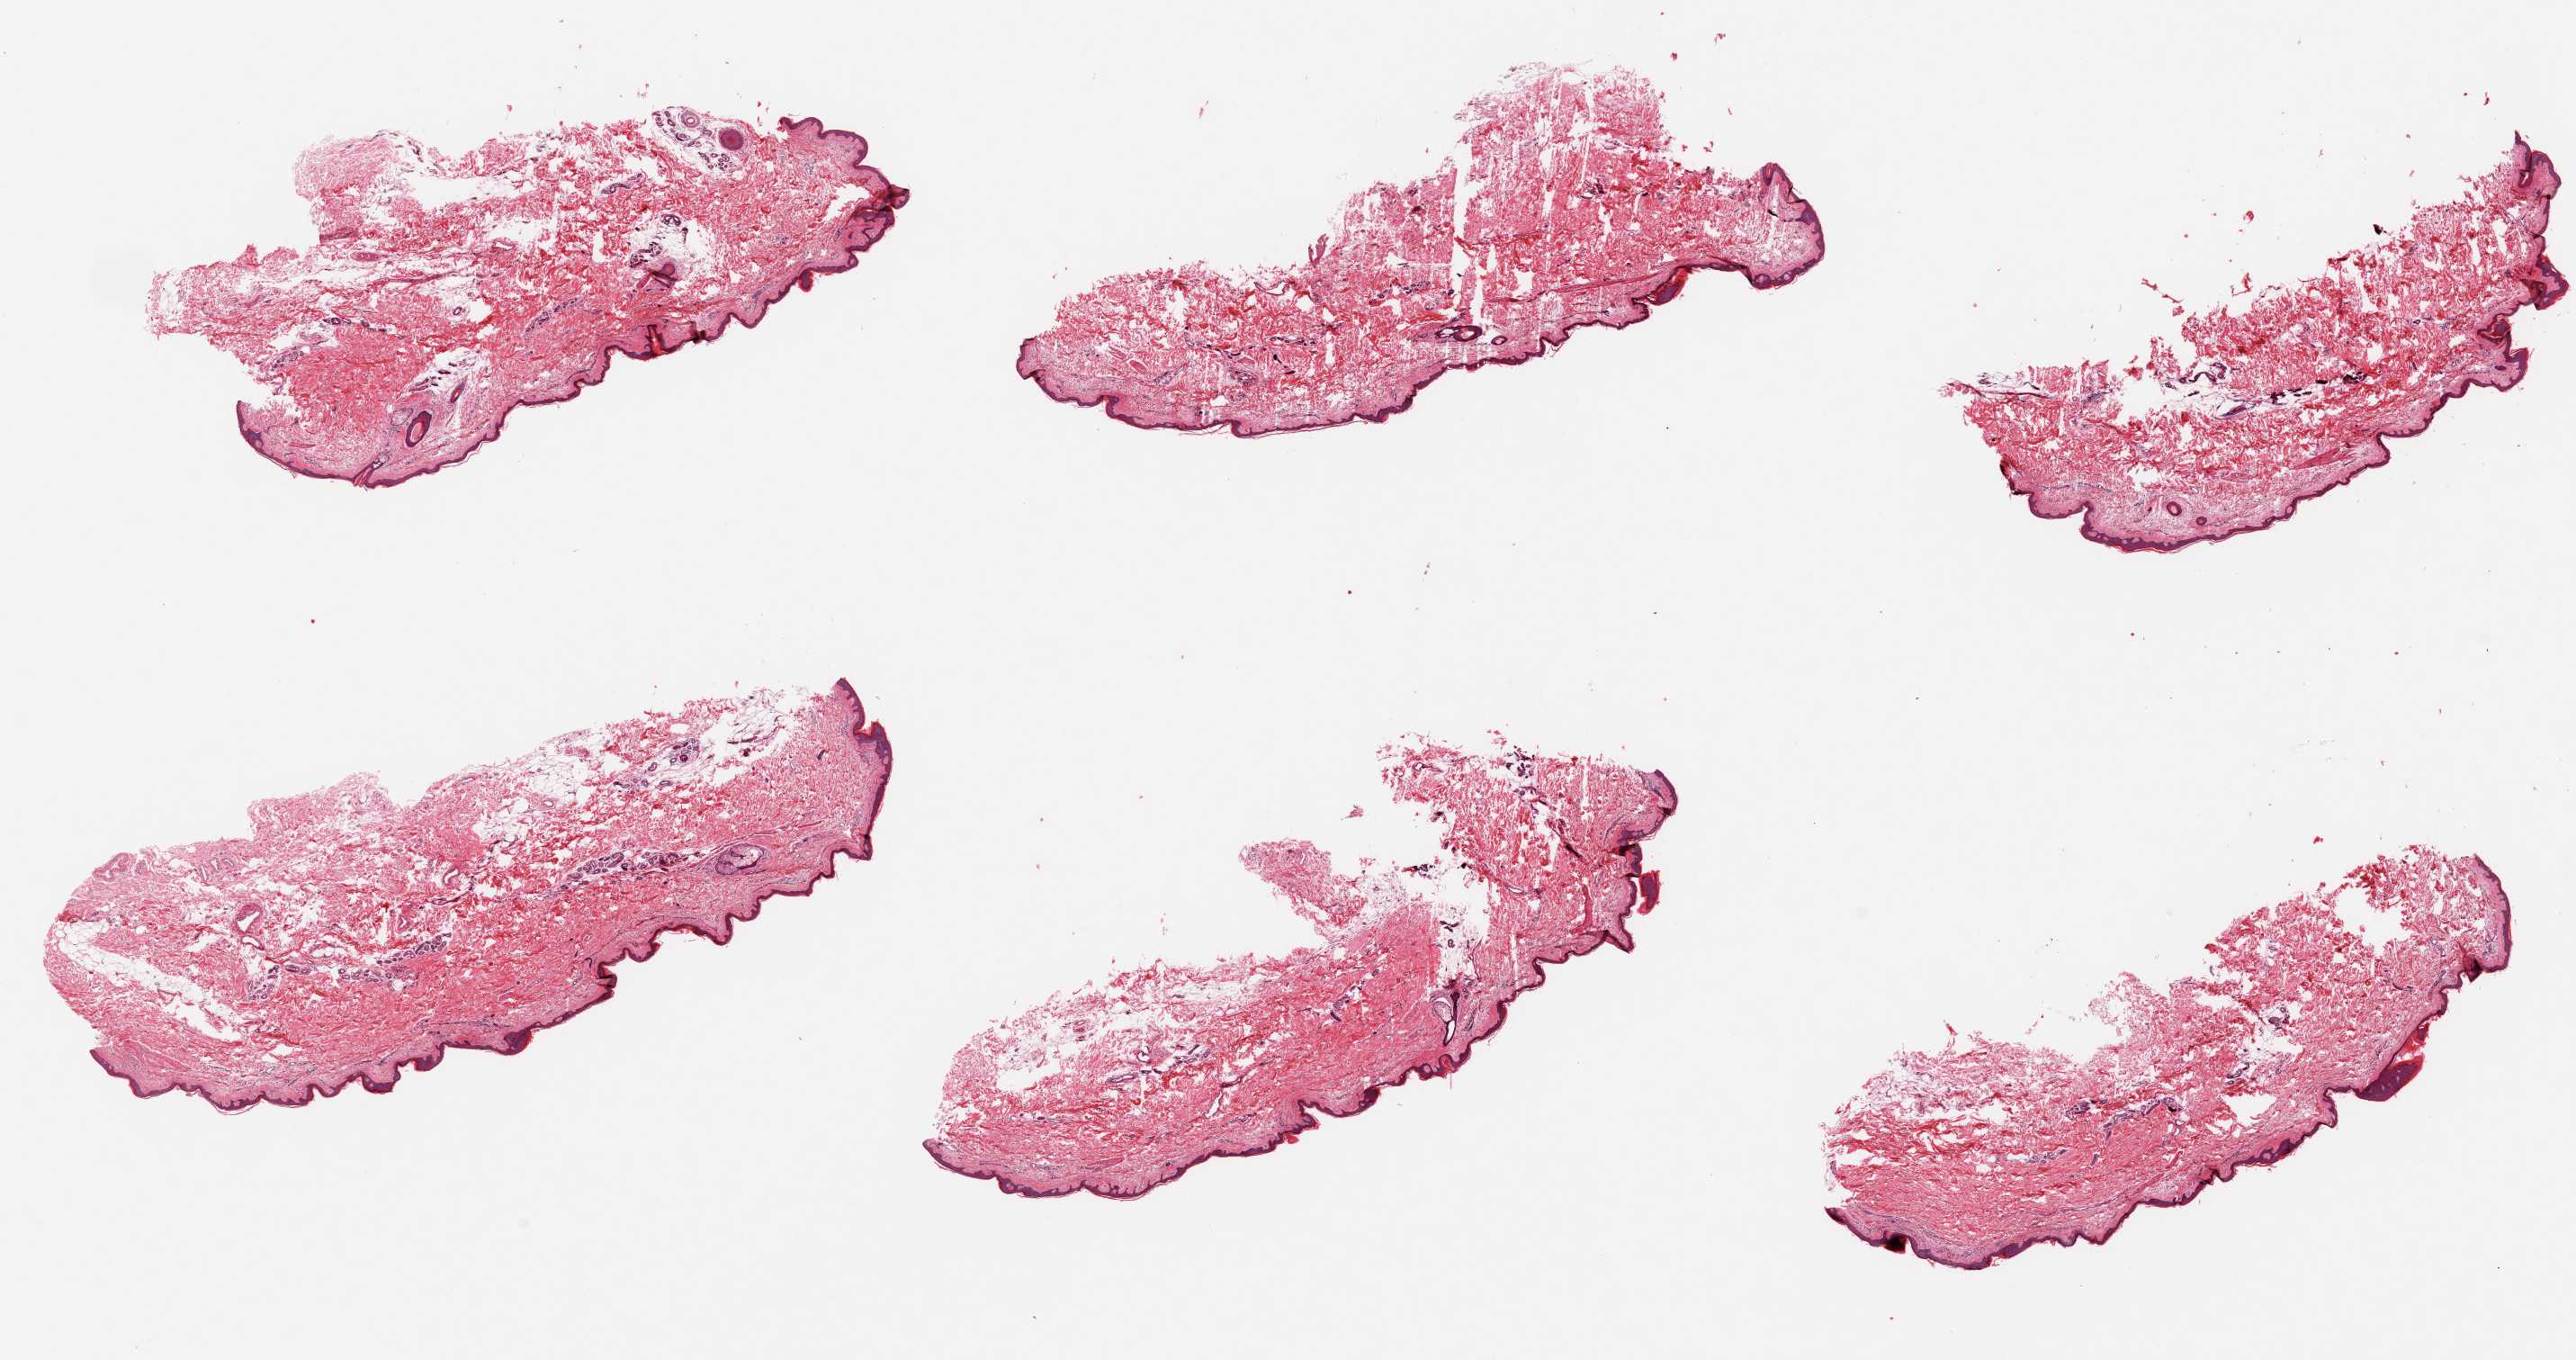
Whole-slide image, H&E stain — low-resolution overview of the scanned area, about 22.6 x 11.9 mm (slide scanned at 20x). PAXgene-fixed, paraffin-embedded tissue. Sampled site (target tissue): skin of lower leg. Donor tissue sample. Donor sex: male.
* pathologist's review note for this sample: 6 pieces; benign keratosis and 20% to 40% intradermal fat and empty spaces, ~34 microns thick epidermis